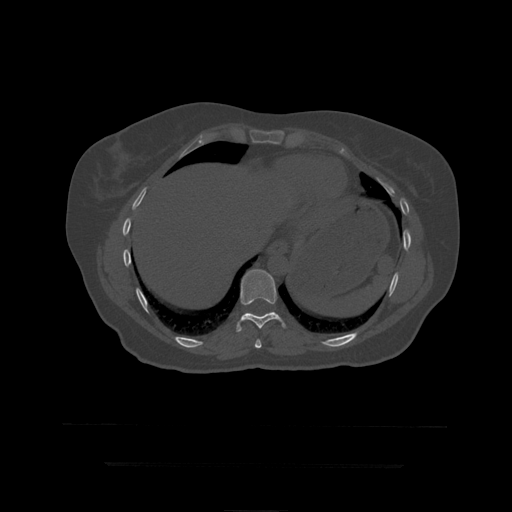
CT including the spine, one axial slice; slice 240 of 399 in the series (ordered by position); reconstruction kernel STANDARD; 120 kVp; bone window (W 1800 / L 400 HU); 1.25 mm slice thickness; 512 × 512 image matrix, field of view 450 × 450 mm. Patient age 41 years. Case-level facts recorded for this patient, not image findings: primary cancer: breast.
Outlined on this slice (semi-automatic segmentation, software-assisted and operator-edited):
- T10 vertebra: bounding box [x1, y1, x2, y2] px = [236, 270, 286, 332]
- T9 vertebra: [255, 339, 262, 350]